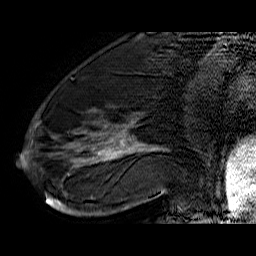
Breast MRI (dynamic contrast-enhanced), one sagittal slice. Slice 20 of 60 in the series (ordered by position). Dynamic contrast-enhanced series, time point 2 of 6 at this slice position (early post-contrast). 1.5 T. TE 6.4 ms, TR 32.9 ms. 4 mm slice thickness. 256 × 256 image matrix, field of view 200 × 200 mm. Female patient. From the clinical record (not read from this slice): setting: breast cancer imaged before/during neoadjuvant chemotherapy; receptor status: HR-positive, HER2-negative.
Annotated regions visible in this slice (semi-automatic segmentation, software-assisted and operator-edited):
- analysis volume of interest (the breast-tissue region the enhancement analysis was run in; not a lesion): bounding box (x1, y1, x2, y2) in pixels: (45, 74, 176, 210)
- tumour enhancement mask (voxels above the 100 % enhancement threshold inside the analysis volume of interest): (46, 125, 166, 208)